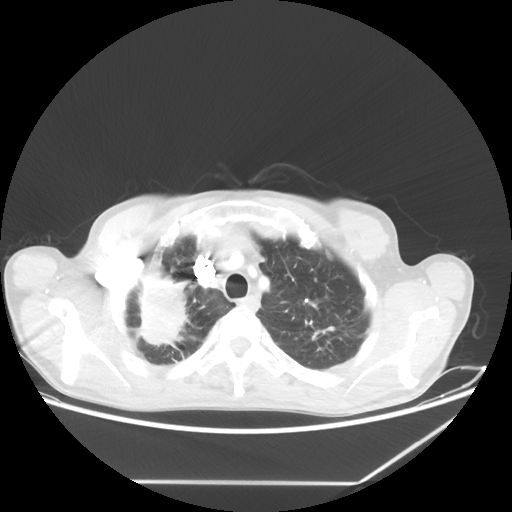
Chest CT, one axial slice. Slice 54 of 65 in the series (ordered by position). Reconstruction kernel STANDARD. 80 kVp. Lung window (W 1500 / L -600 HU). 512 × 512 image matrix, field of view 397 × 397 mm. Patient: male, 68 years. From the clinical record (not read from this slice): clinical TNM (as recorded): T3 N3 M0.
Structures marked on this image (rectangle marked by the reading radiologist):
- lung tumour (recorded histology: adenocarcinoma): bounding box [x1, y1, x2, y2] px = [125, 254, 193, 353]